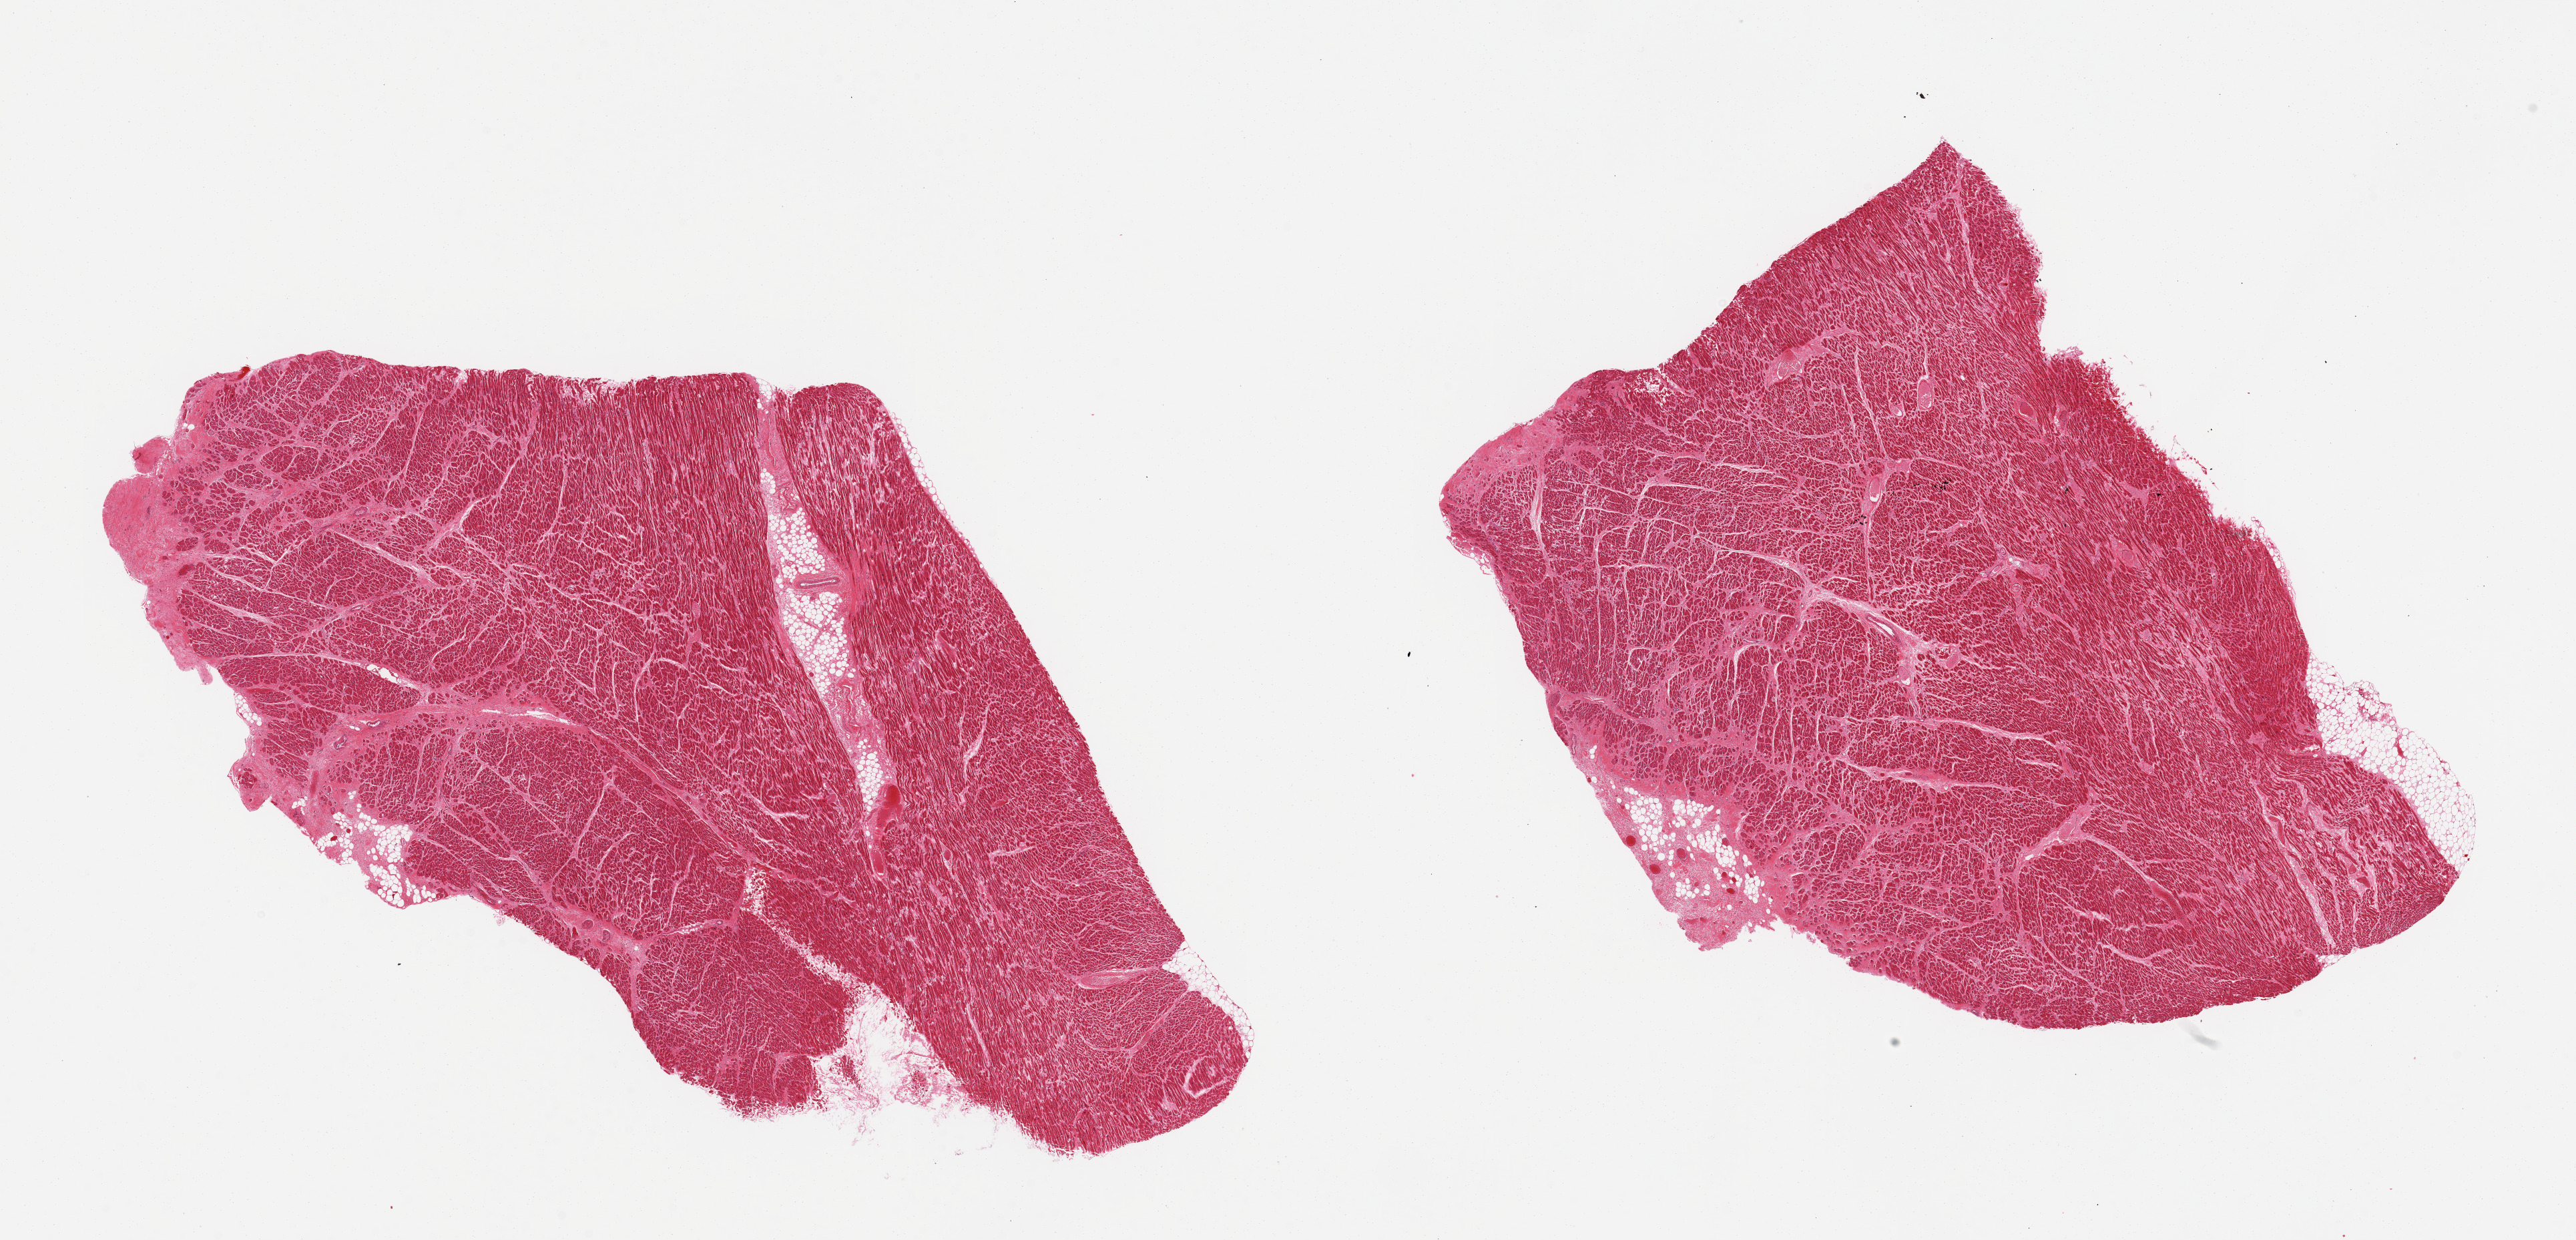
Digitized H&E-stained section, low-resolution overview of the scanned area, about 30.5 x 14.7 mm. PAXgene-fixed paraffin-embedded (PFPE) section. Target tissue: heart. Tissue donor sample. Donor: male.
Review note (as recorded): 2 pieces, small component of fat (<10% both pieces), increased interstitial and patchy fibrosis with evidence of old myocardial infarction, myocyte hypertrophy.